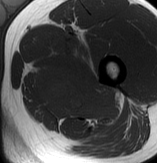
MRI of an extremity soft-tissue mass, one axial slice; MR volume resampled by the dataset authors to the PET/CT grid (not the native acquisition matrix); 157 × 163 image matrix. Male patient. From the clinical record (not read from this slice): histological type: extraskeletal osteosarcoma; grade: high; site of the primary tumour: left adductur.
Annotated regions visible in this slice (expert contour drawn on MRI and transferred to this co-registered scan by the dataset authors):
- gross tumour volume (mass): bounding box [x1, y1, x2, y2] px = [31, 35, 121, 121]